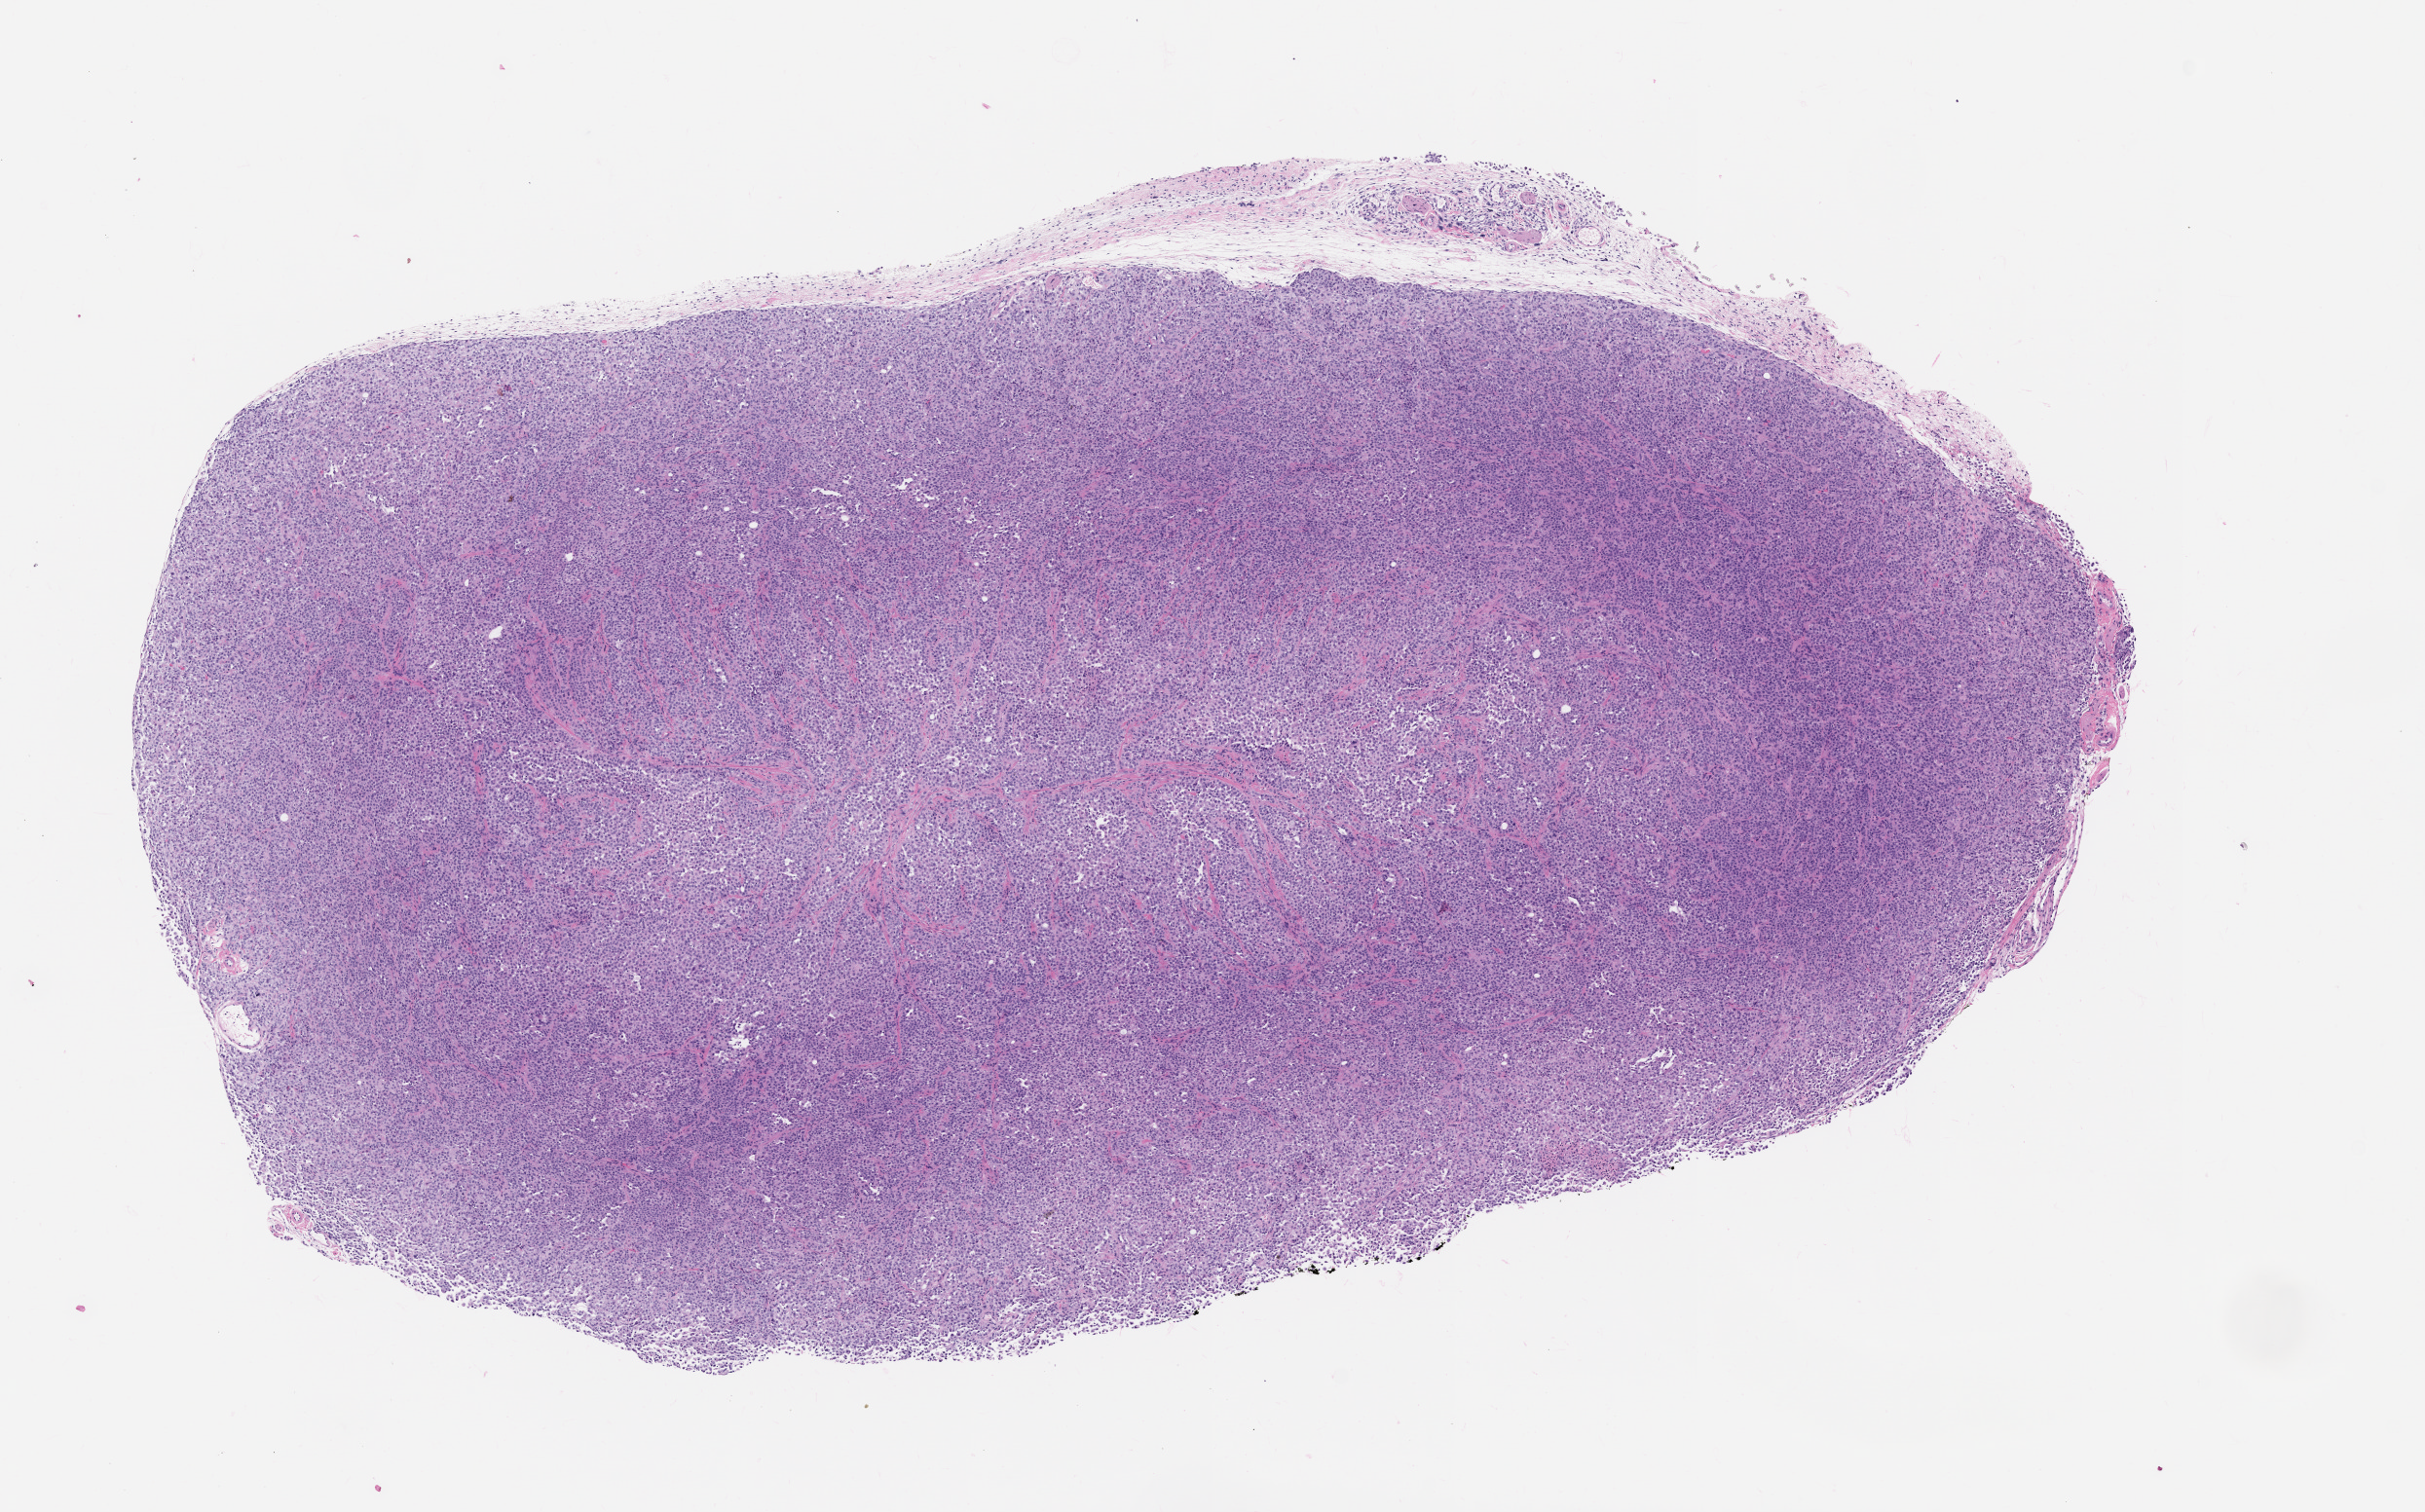
Hematoxylin and eosin (H&E) whole-slide image of a patient-derived xenograft (PDX) tumor grown in a mouse, passage 1, low-resolution overview of the scanned area, about 10.0 x 6.2 mm. FFPE section.
• originating patient diagnosis: Mesothelial Neoplasm